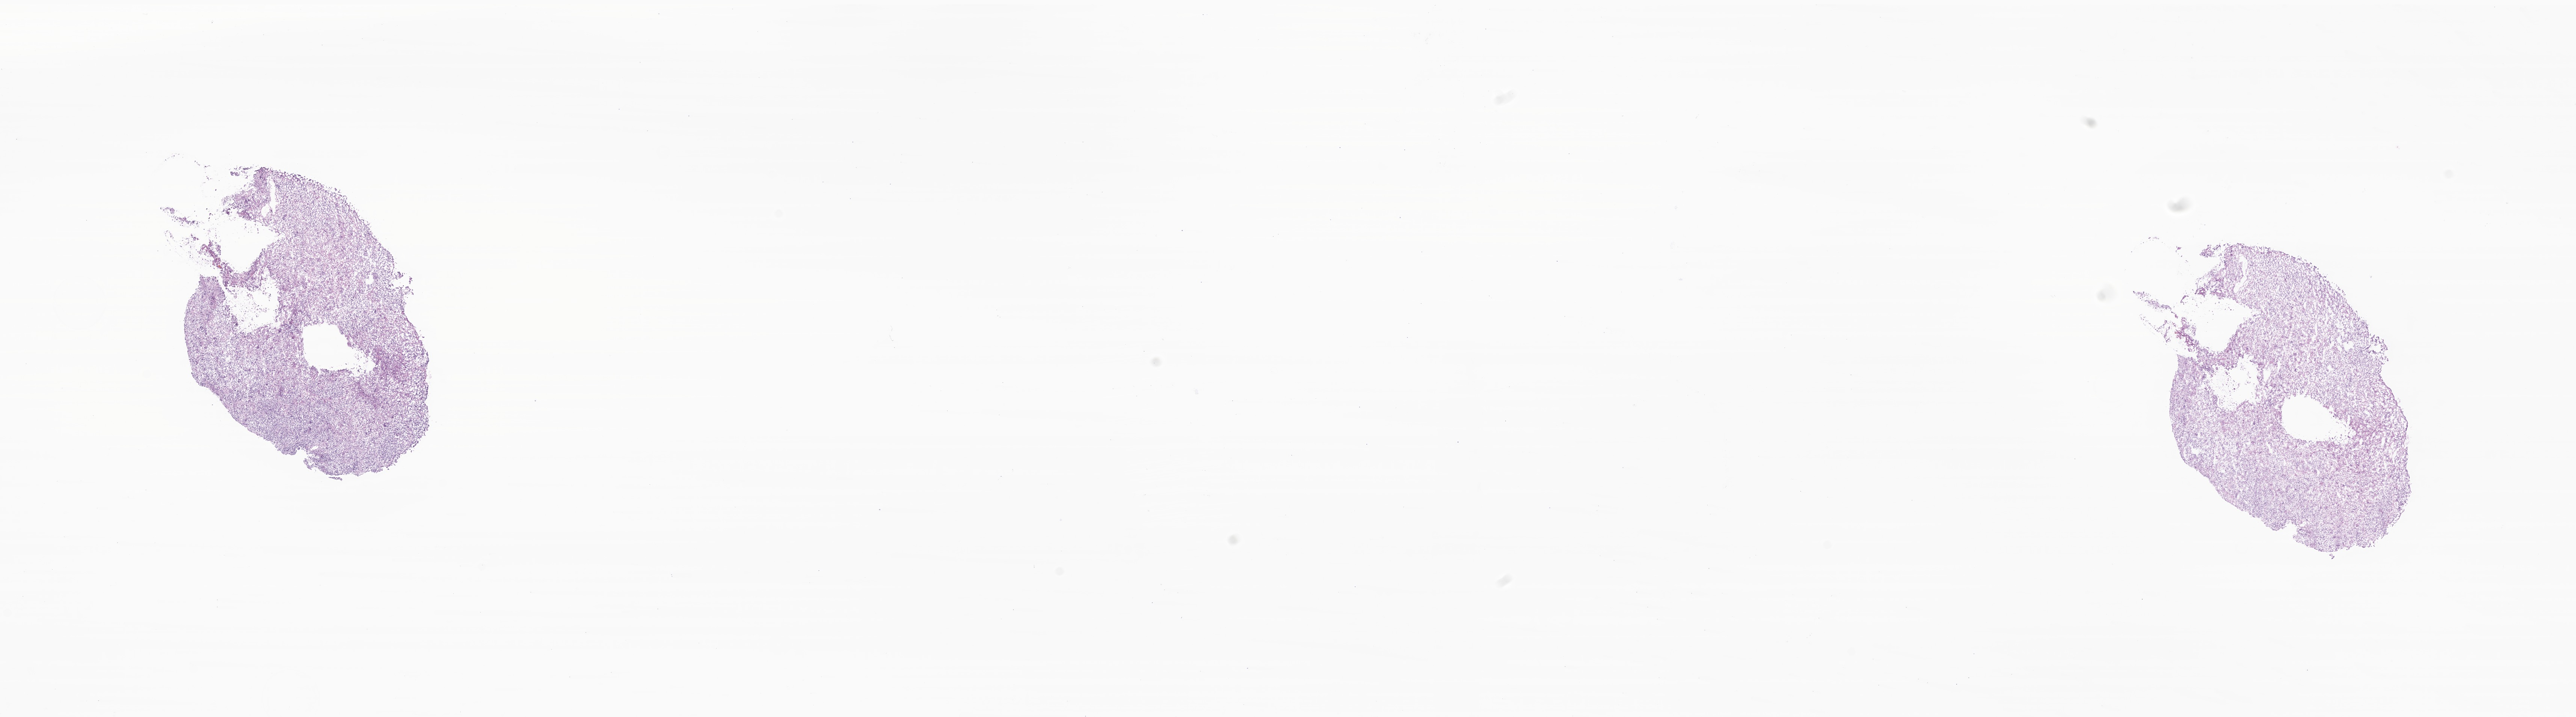
Whole-slide image, haematoxylin and eosin stain of tumor tissue from the brain — whole scanned area (about 28.9 x 8.0 mm) shown as a low-resolution overview, cryosection (OCT / tissue freezing medium). Female patient, age 205 months.
Diagnosis: Glioma, malignant.